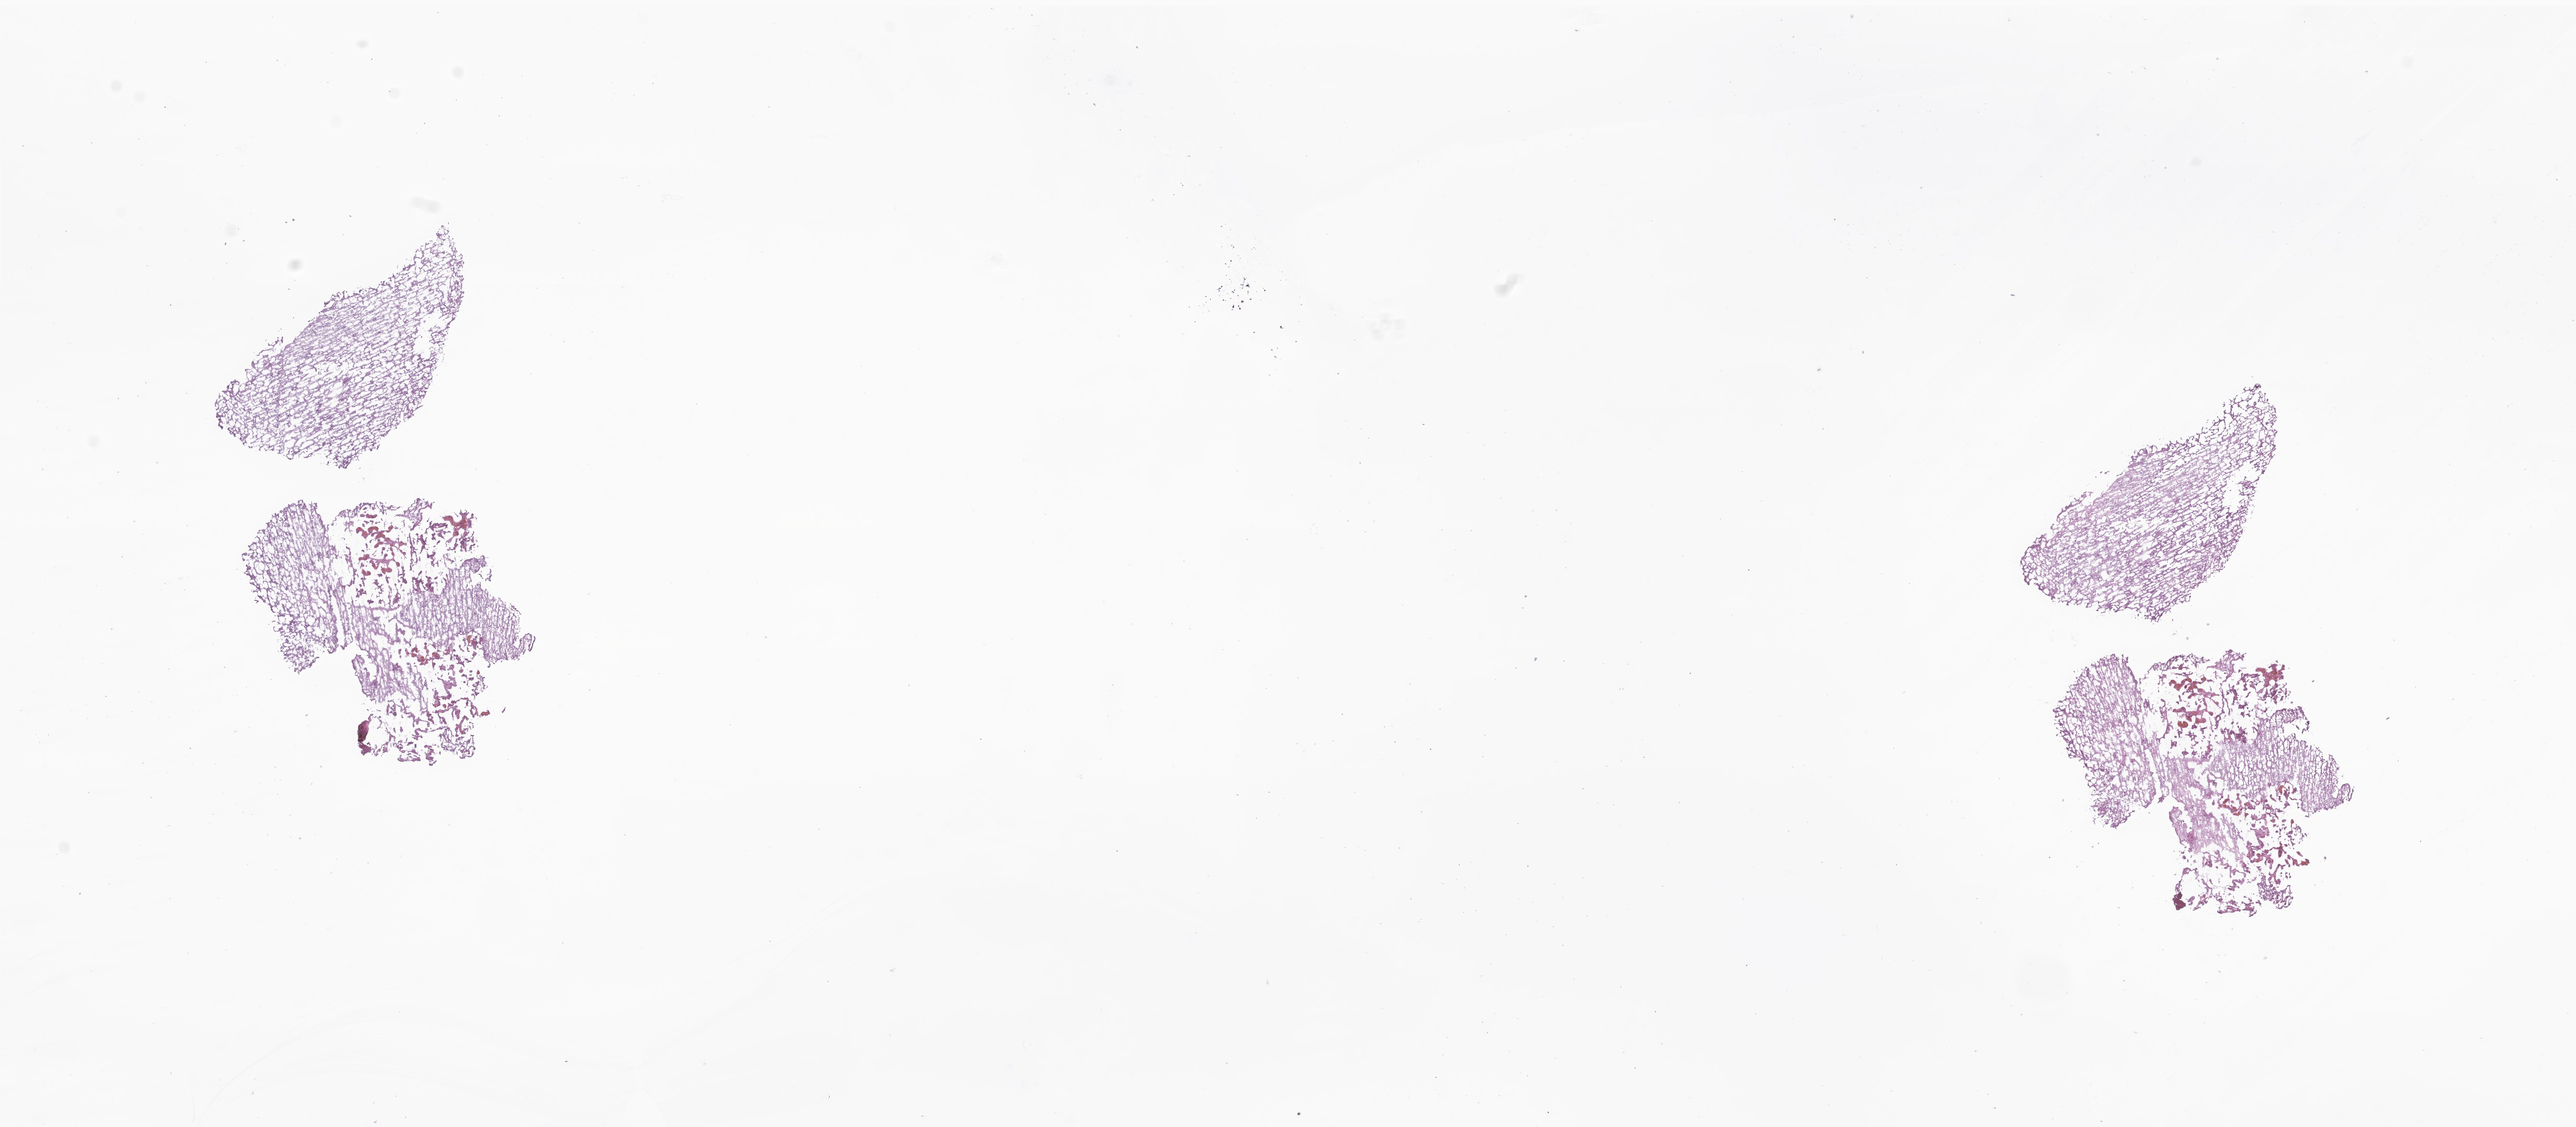
Digitized hematoxylin and eosin (H&E)-stained section of tumor tissue from the brain, a low-resolution overview of the entire scanned area, about 22.7 x 9.9 mm, frozen section. Patient: male, age 893 days (about 2.4 years).
Diagnosis (ICD-O-3 morphology term): Ependymoma, NOS.